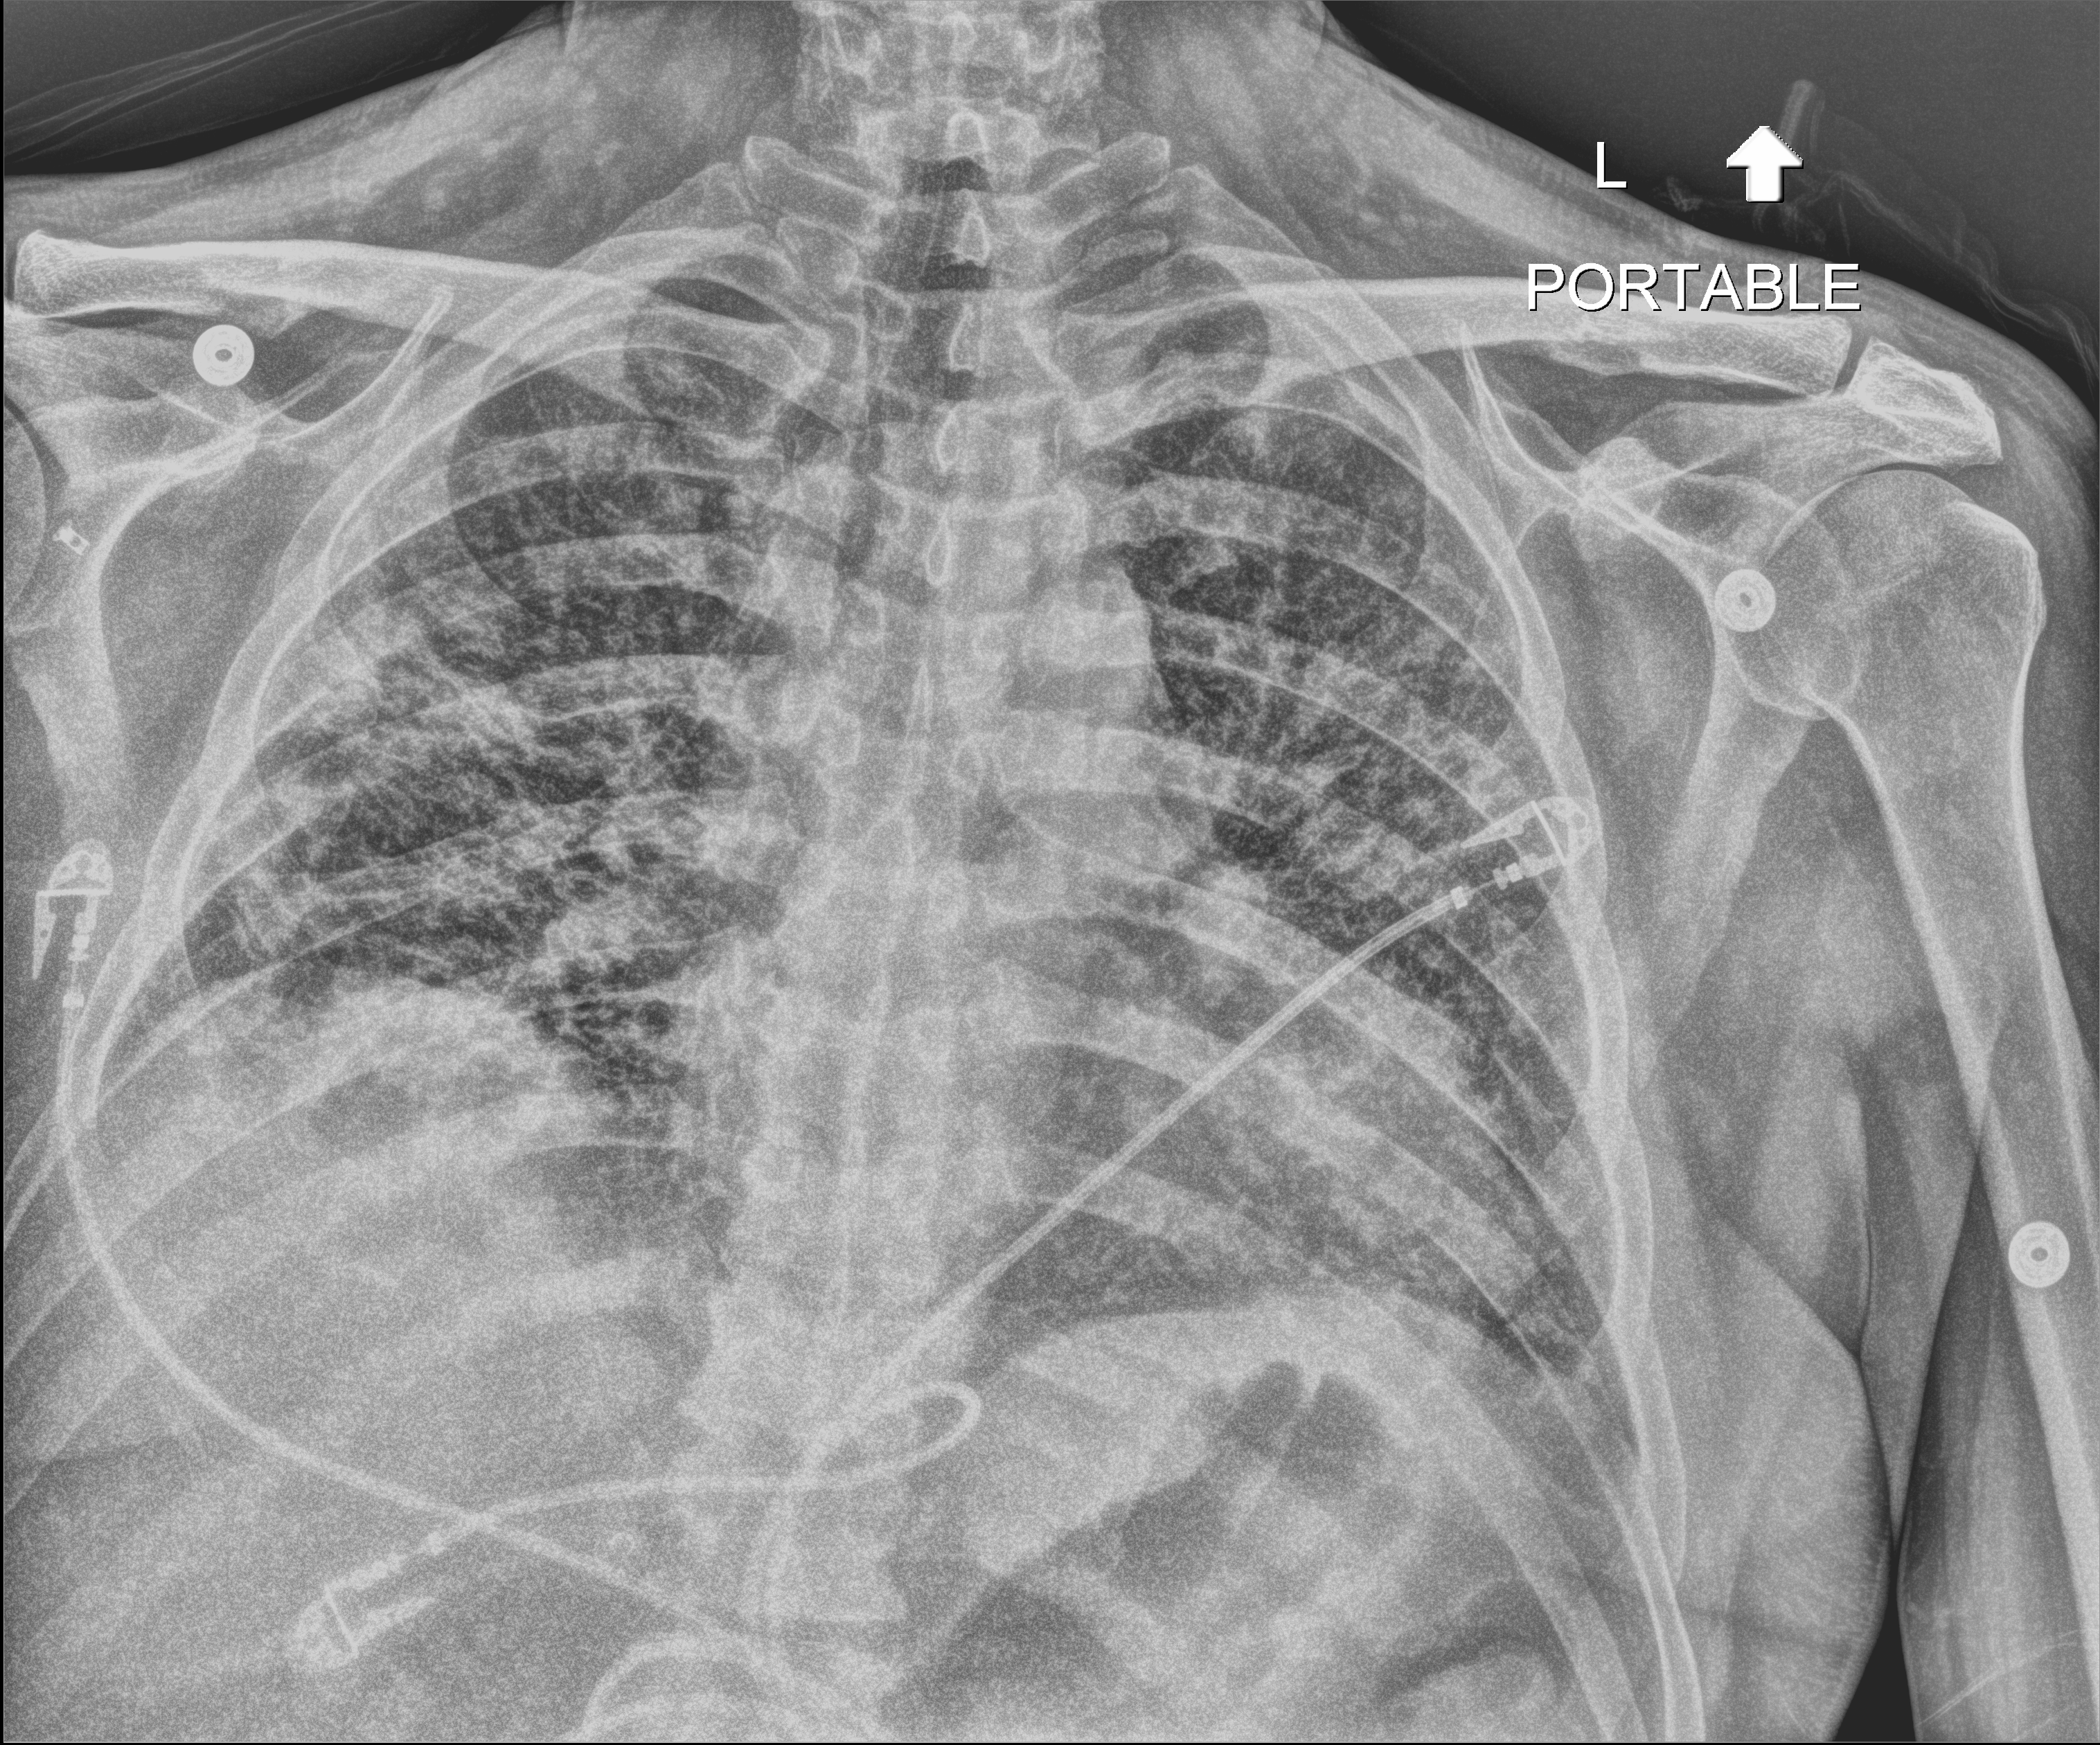
Portable chest radiograph, anteroposterior (AP) projection. Male patient hospitalised with COVID-19, age 18–59 years.
Hospital-stay facts (about this admission, not read from this image; timing relative to this image not recorded): length of hospital stay: 52 days.